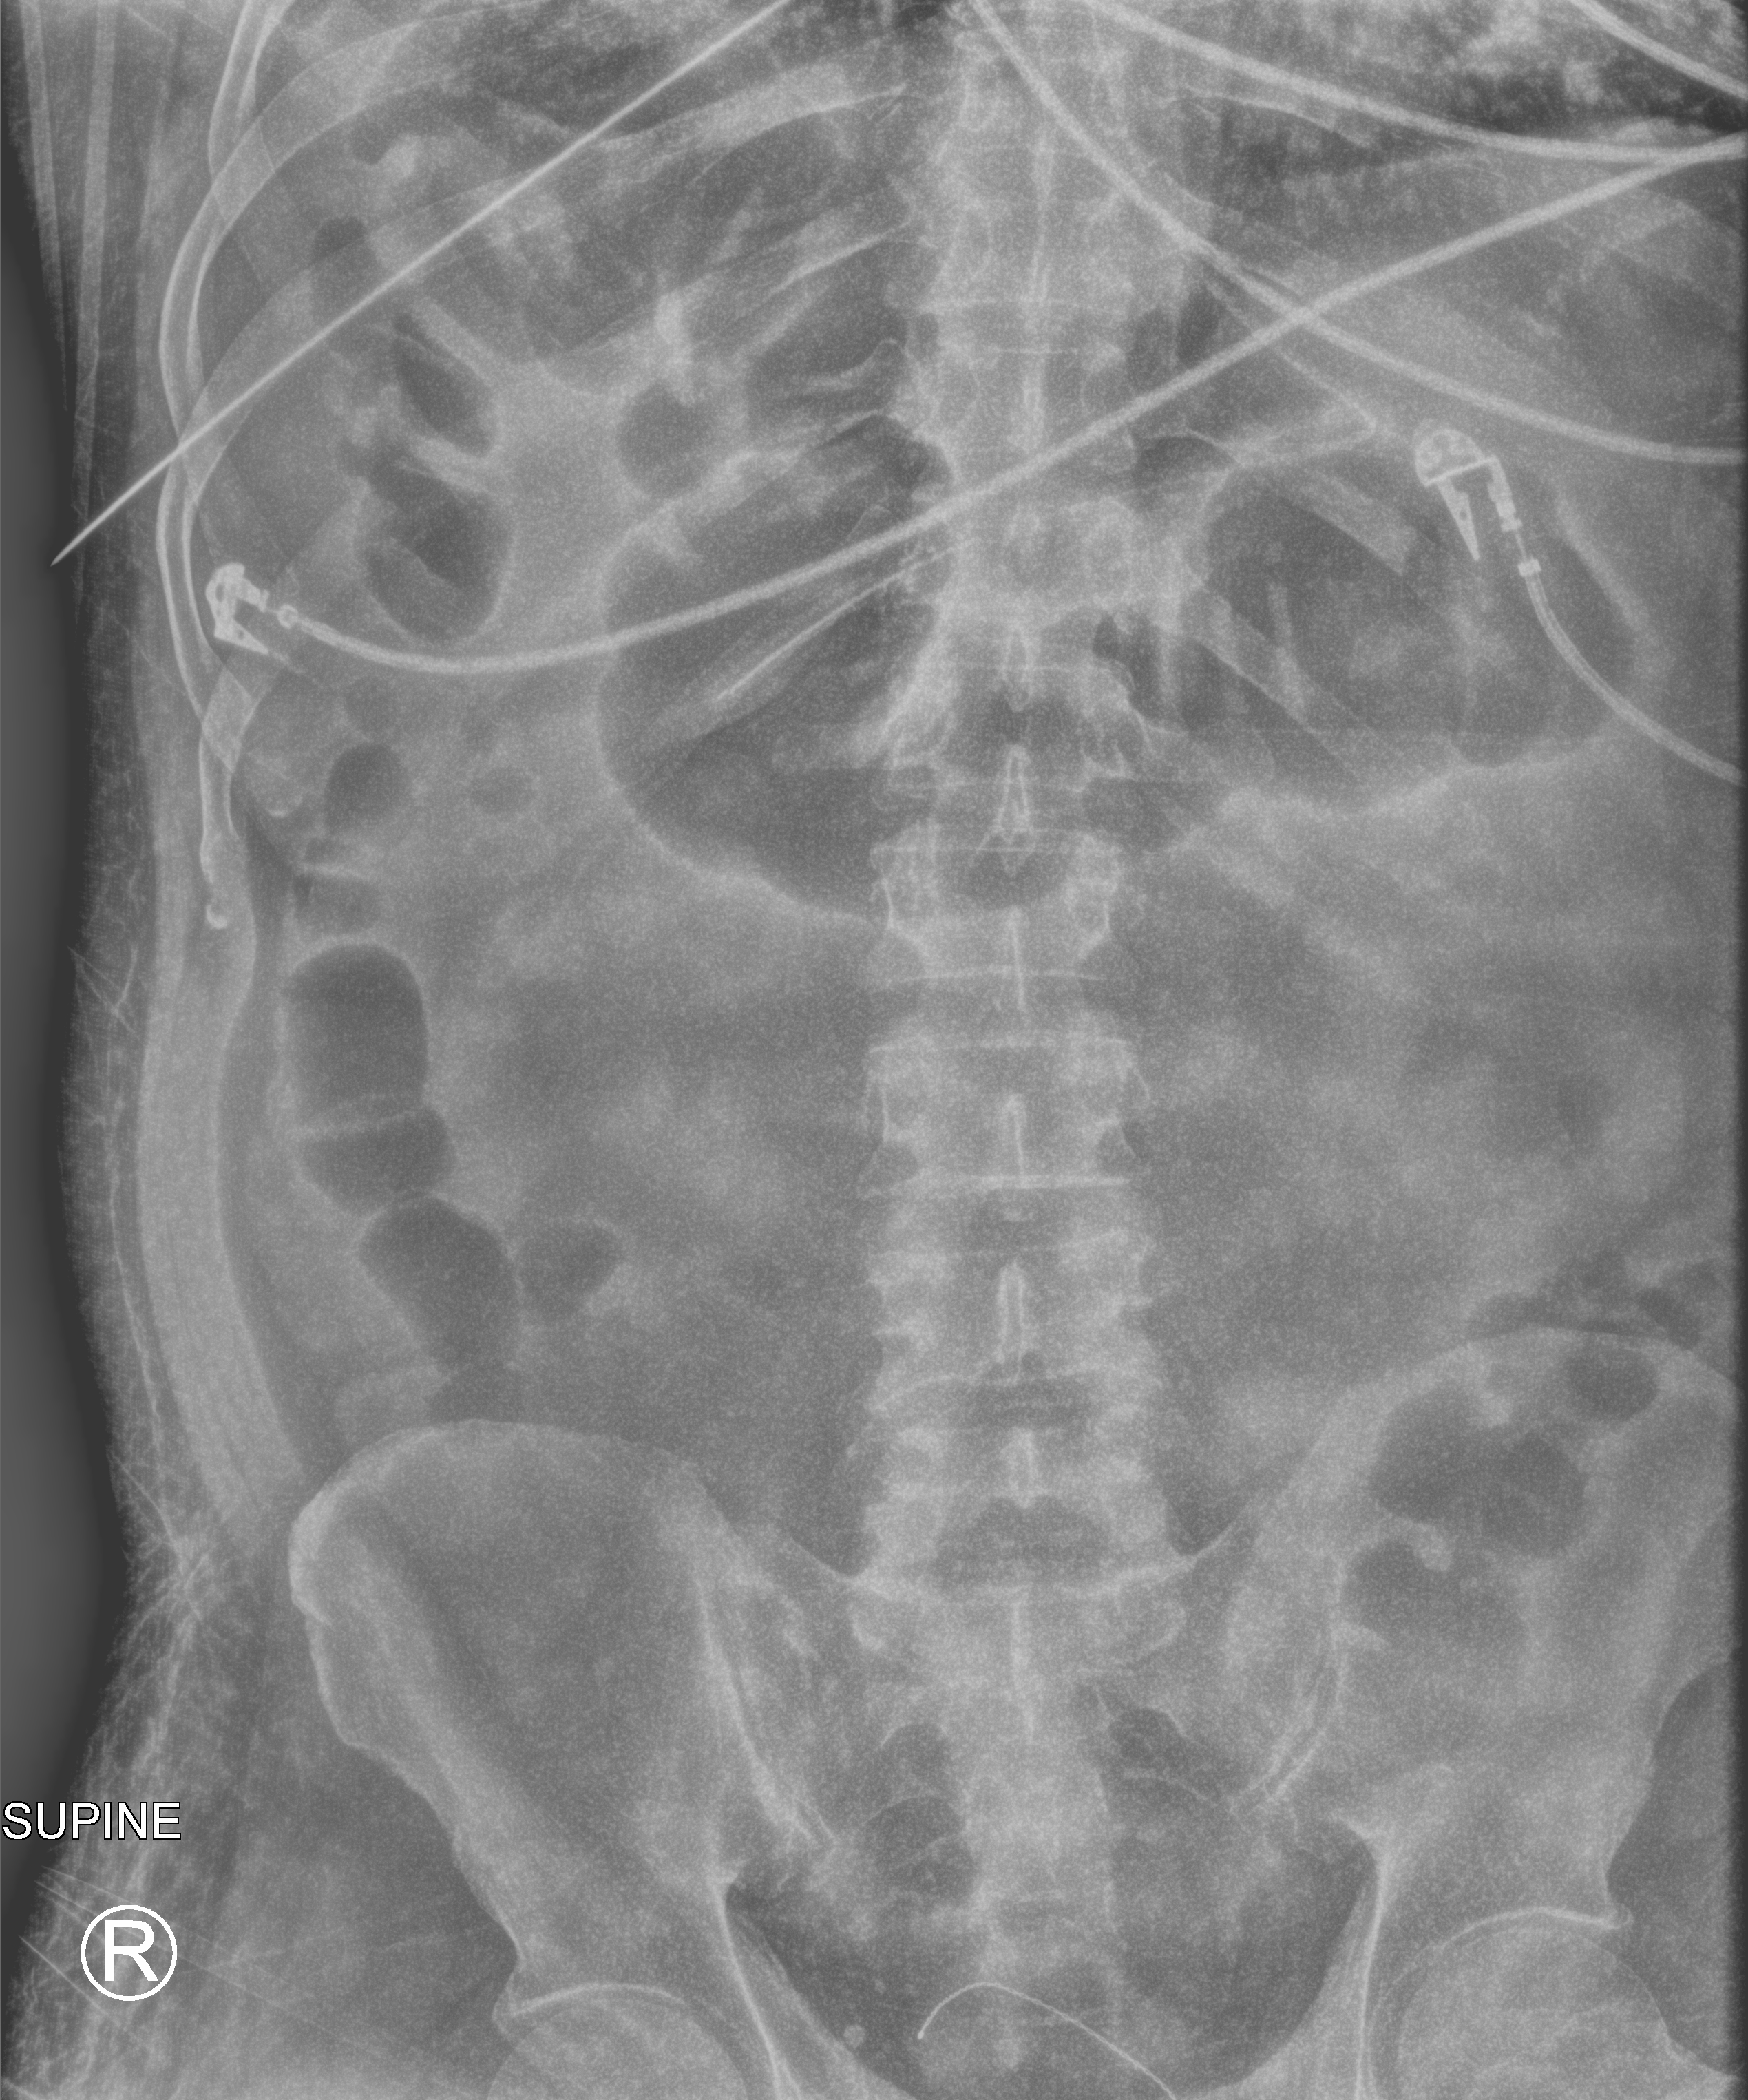
Abdomen X-ray (portable). Patient hospitalised with COVID-19; male, aged 18–59 years.
Hospital-stay facts (about this admission, not read from this image; timing relative to this image not recorded):
- hypertension (admission record): no